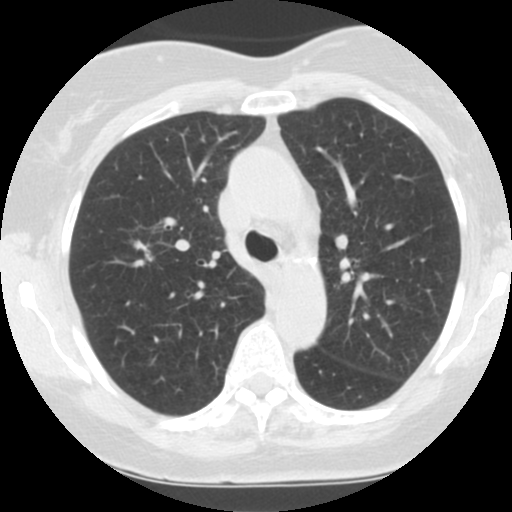
Low-dose screening chest CT, one axial slice; position 74 of 106 along the scan axis; reconstruction kernel STANDARD; 120 kVp; one of 2 acquisitions stored at this slice position; lung window (W 1500 / L -600 HU); 2.5 mm slice thickness; 512 × 512 image matrix, field of view 280 × 280 mm.
Annotated regions visible in this slice (expert manual segmentation):
- lesion 1 (tumor, upper lobe of right lung): bounding box (x1, y1, x2, y2) in pixels: (137, 243, 145, 249)